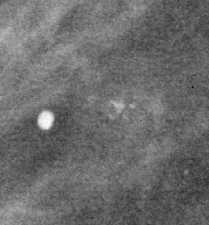
Cropped region of a digitized screen-film mammogram centred on a radiologist-marked abnormality, right breast, MLO view.
Finding: calcifications, morphology amorphous / pleomorphic, distribution clustered; BI-RADS assessment category 4; pathology result (as recorded, not read from the image): benign.